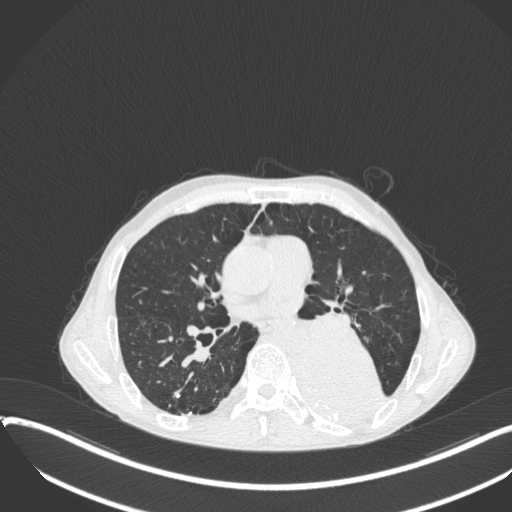
Chest CT, one axial slice. Slice 193 of 400 in the series (ordered by position). Reconstruction kernel B31f. 120 kVp. Lung window (W 1500 / L -600 HU). 1 mm slice thickness. 512 × 512 image matrix, field of view 400 × 400 mm. Male patient, age 57 years. Case-level facts recorded for this patient, not image findings: clinical TNM (as recorded): T4 N0 M0.
Outlined on this slice (bounding box drawn by a radiologist):
- lung tumour (recorded histology: squamous cell carcinoma): bounding box (x1, y1, x2, y2) in pixels: (287, 327, 387, 421)